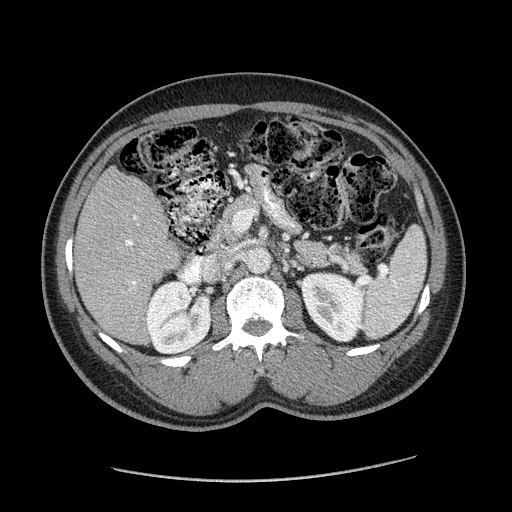
Contrast-enhanced abdominal CT (liver protocol), one axial slice. Position 81 of 182 along the scan axis. 120 kVp. Soft-tissue window (W 400 / L 40 HU). 2.5 mm slice thickness. 512 × 512 image matrix, field of view 400 × 400 mm. Case-level facts recorded for this patient, not image findings: diagnosis: hepatocellular carcinoma (patient treated with transarterial chemoembolisation; whether this scan precedes or follows treatment is not stated here); TNM stage (as recorded): Stage-I; Child-Pugh class: A; tumour differentiation: well differentiated; tumour size: 3.1 cm.
Structures marked on this image (semi-automatically segmented with operator editing):
- liver parenchyma outside the tumour (the mass and vessels are separate outlines, so this box may not span the whole liver): bounding box [x1, y1, x2, y2] px = [76, 166, 180, 344]
- liver vessels: [125, 215, 144, 291]